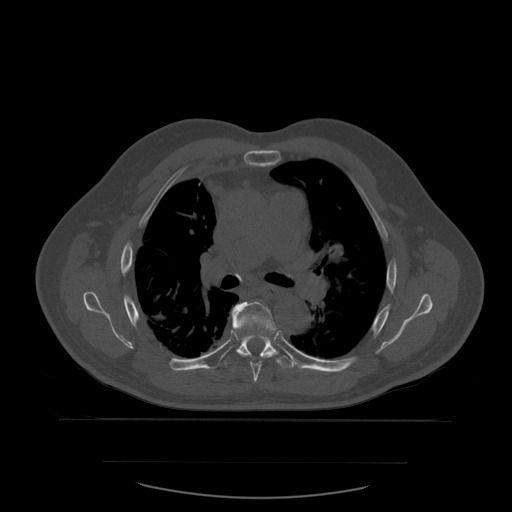
CT including the spine, one axial slice. Position 395 of 590 along the scan axis. Bone window (W 1800 / L 400 HU). 1.25 mm slice thickness. 512 × 512 image matrix, field of view 479 × 479 mm. Patient age 71 years. From the clinical record (not read from this slice): primary cancer: lung; vertebrae with lytic lesions (as recorded): T1, T2, L5, S1.
Outlined on this slice (semi-automatic segmentation, software-assisted and operator-edited):
- T6 vertebra: bounding box <232,302,277,384> (left, top, right, bottom; pixels)
- T7 vertebra: <223,304,295,369>